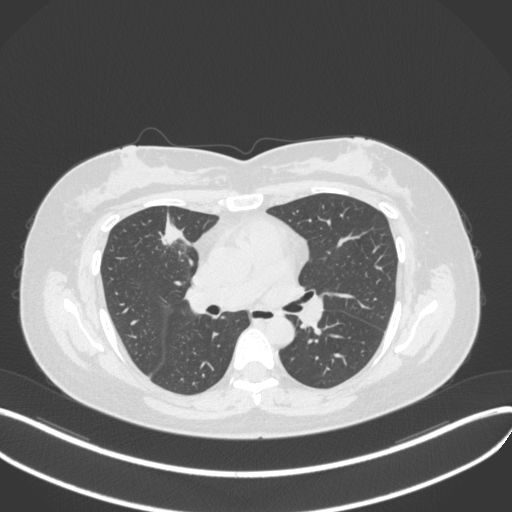
Chest CT, one axial slice. Position 178 of 272 along the scan axis. Reconstruction kernel B31f. Lung window (W 1500 / L -600 HU). 512 × 512 image matrix, field of view 400 × 400 mm. Patient: female, 42 years. From the clinical record (not read from this slice): clinical TNM (as recorded): T1b N0 M0.
Structures marked on this image (rectangle marked by the reading radiologist):
- lung tumour (recorded histology: adenocarcinoma): bounding box (x1, y1, x2, y2) in pixels: (158, 215, 183, 250)